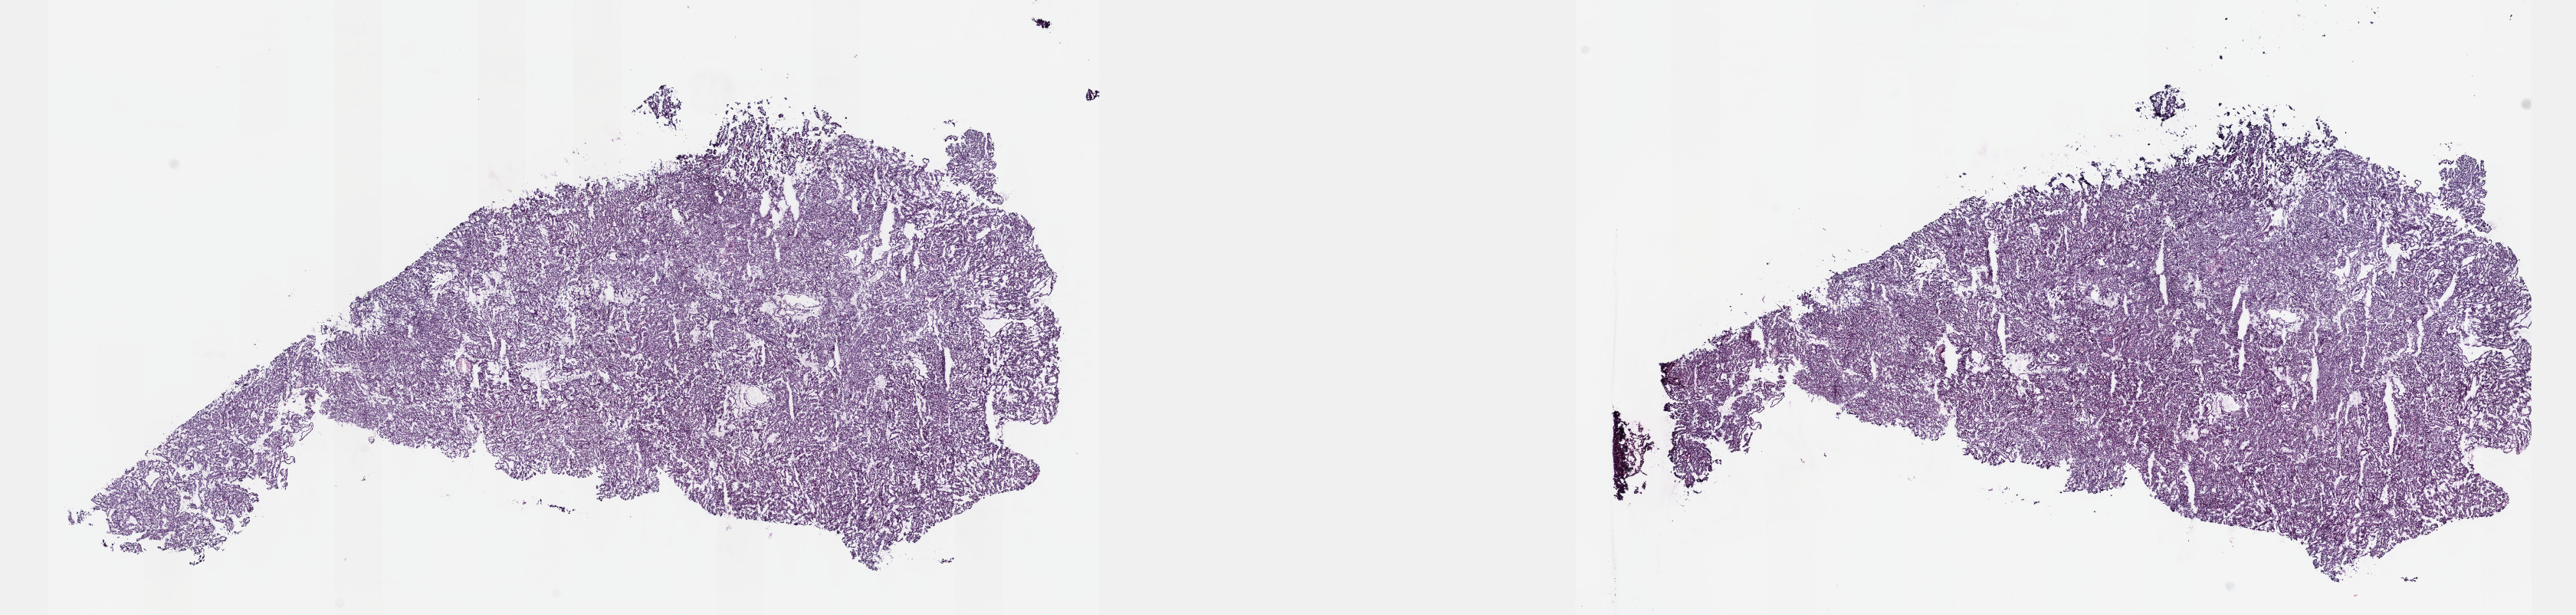
Digitized H&E tissue section (whole slide), shown as a low-resolution overview of the whole scanned area (about 27.2 x 6.5 mm), frozen section, kidney, primary tumour sample. Patient: male, age at initial diagnosis 65 years. Composition of this section per pathologist review: tumour cells 90%, tumour nuclei 95%, normal cells 0%, stromal cells 10%, necrosis 0%. Infiltration values recorded for this section: lymphocyte infiltration 0%, monocyte infiltration 0%, neutrophil infiltration 0%.
AJCC pathologic stage: I (6th edition). Laterality: left. Pathologic diagnosis: Papillary adenocarcinoma, NOS.